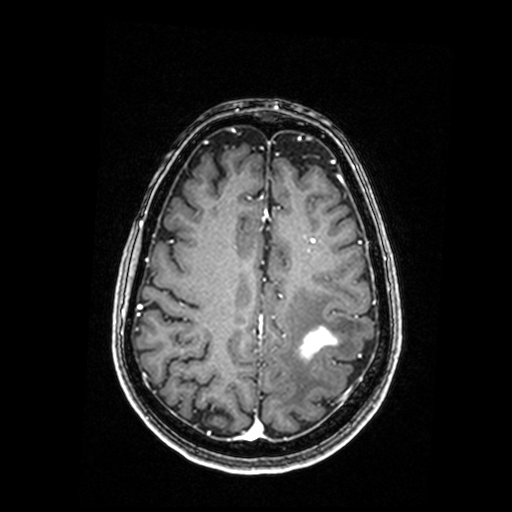
Brain MRI from a brain-tumour surgery series, one axial slice. Slice 63 of 192 in the series (ordered by position). T1-weighted post-contrast. 0.98 mm slice thickness. 512 × 512 image matrix, field of view 250 × 250 mm. From the clinical record (not read from this slice): histopathology: Metastastic Carcinoma, Poorly Differentiated; tumour location: Left Parietal.
Structures marked on this image (outlined manually by an expert reader):
- tumour: bounding box <299,328,337,359> (left, top, right, bottom; pixels)